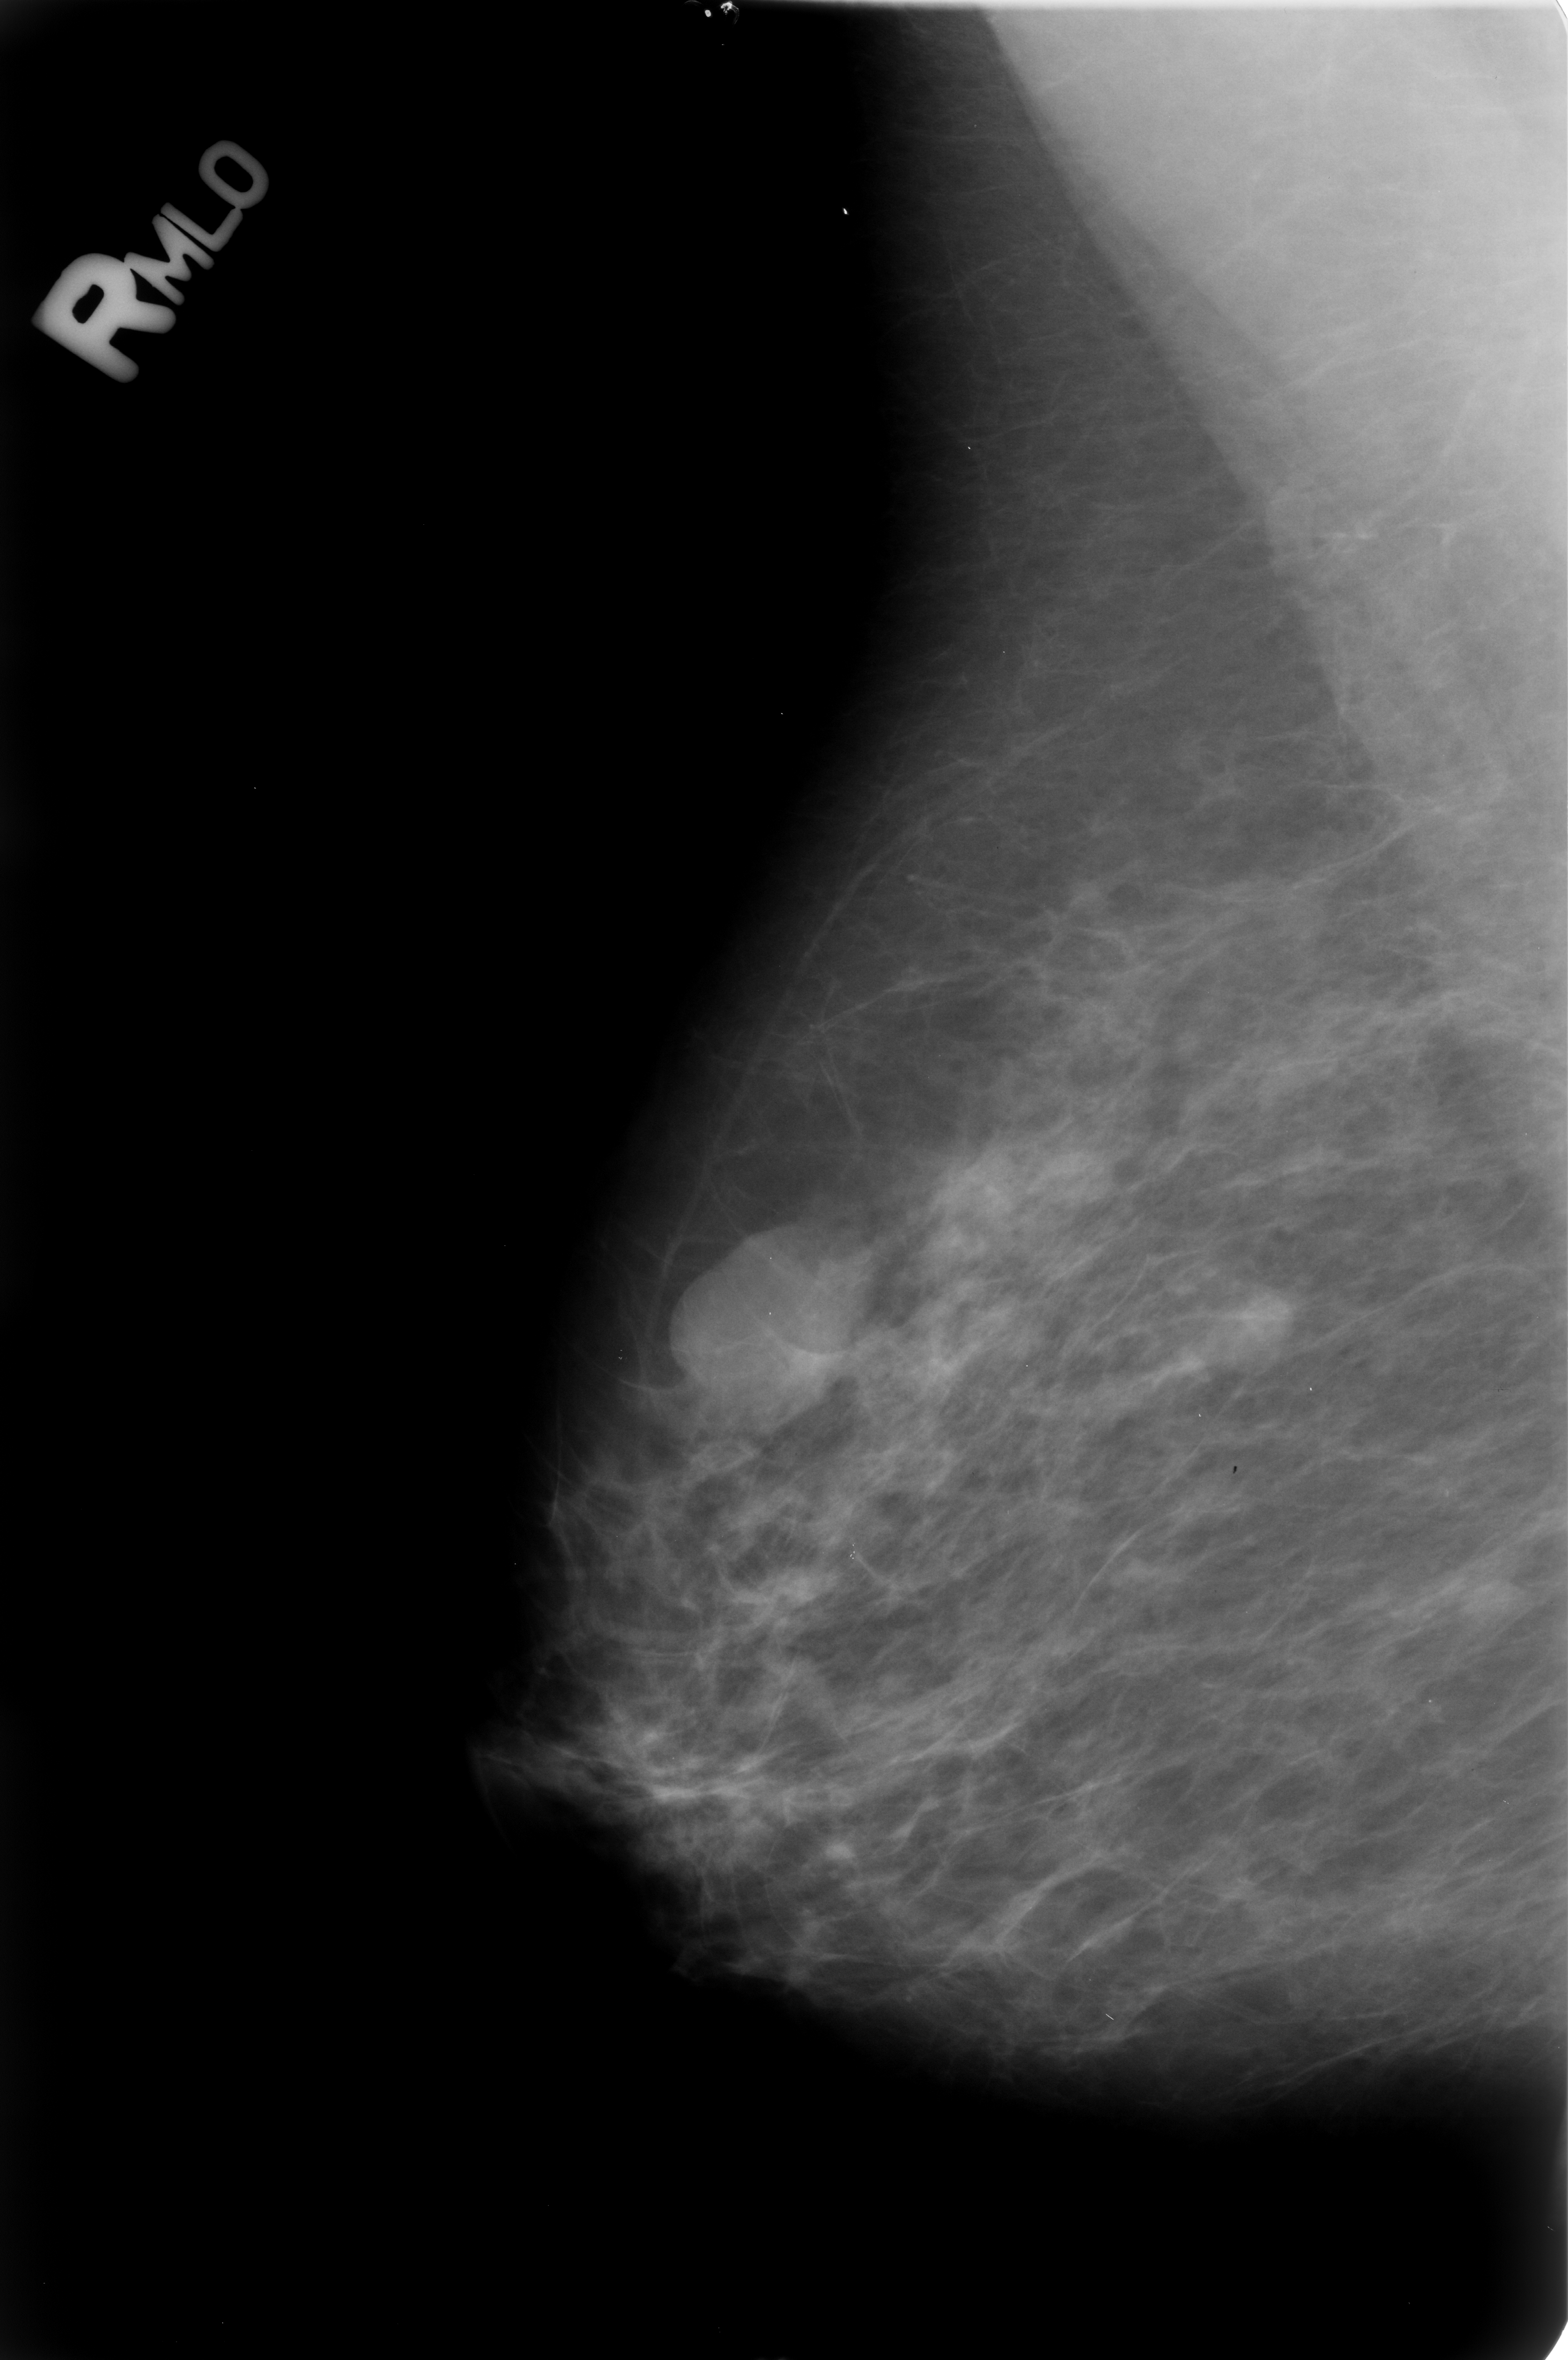
Mammogram (digitized film), right breast, mediolateral oblique (MLO) view, breast composition: scattered fibroglandular densities (BI-RADS density category 2 of 4).
Mass, shape lobulated, margins circumscribed / obscured; BI-RADS assessment category 4; pathology result (as recorded, not read from the image): benign.